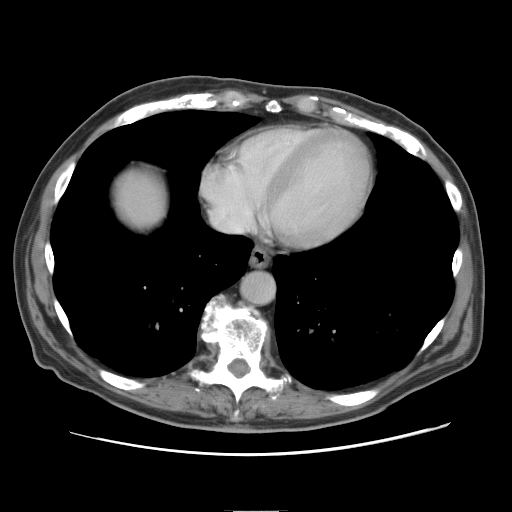
Contrast-enhanced abdominal CT, one axial slice. Position 80 of 89 along the scan axis. 120 kVp. Intravenous contrast given. Soft-tissue window (W 400 / L 40 HU). 5 mm slice thickness. 512 × 512 image matrix. Male patient, age 69 years. From the clinical record (not read from this slice): diagnosis: colorectal cancer liver metastases, imaged before liver resection; multiple liver metastases: no.
Annotated regions visible in this slice (outlined manually by an expert reader):
- liver: box from (x=111, y=166) to (x=166, y=230) px
- planned liver remnant (the part of the liver to remain after resection): (x=112, y=167)–(x=167, y=230)